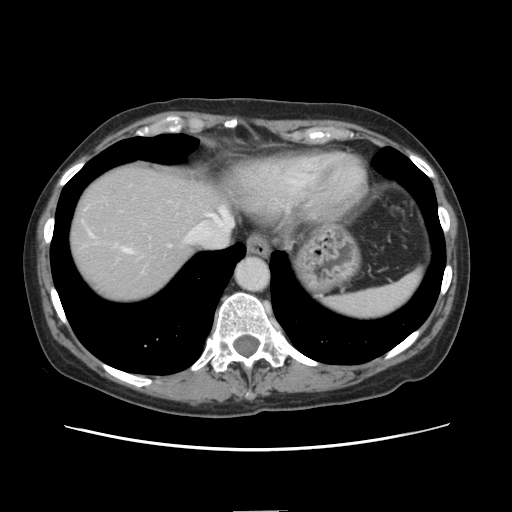
Contrast-enhanced abdominal CT, one axial slice; slice 123 of 141 in the series (ordered by position); intravenous contrast given; soft-tissue window (W 400 / L 40 HU); 2.5 mm slice thickness; 512 × 512 image matrix, field of view 350 × 350 mm. Female patient, age 63 years. From the clinical record (not read from this slice): diagnosis: colorectal cancer liver metastases, imaged before liver resection; multiple liver metastases: yes.
Outlined on this slice (manually delineated by an expert):
- hepatic veins: box from (x=124, y=209) to (x=232, y=252) px
- liver: (x=69, y=162)–(x=297, y=304)
- planned liver remnant (the part of the liver to remain after resection): (x=207, y=188)–(x=232, y=227)